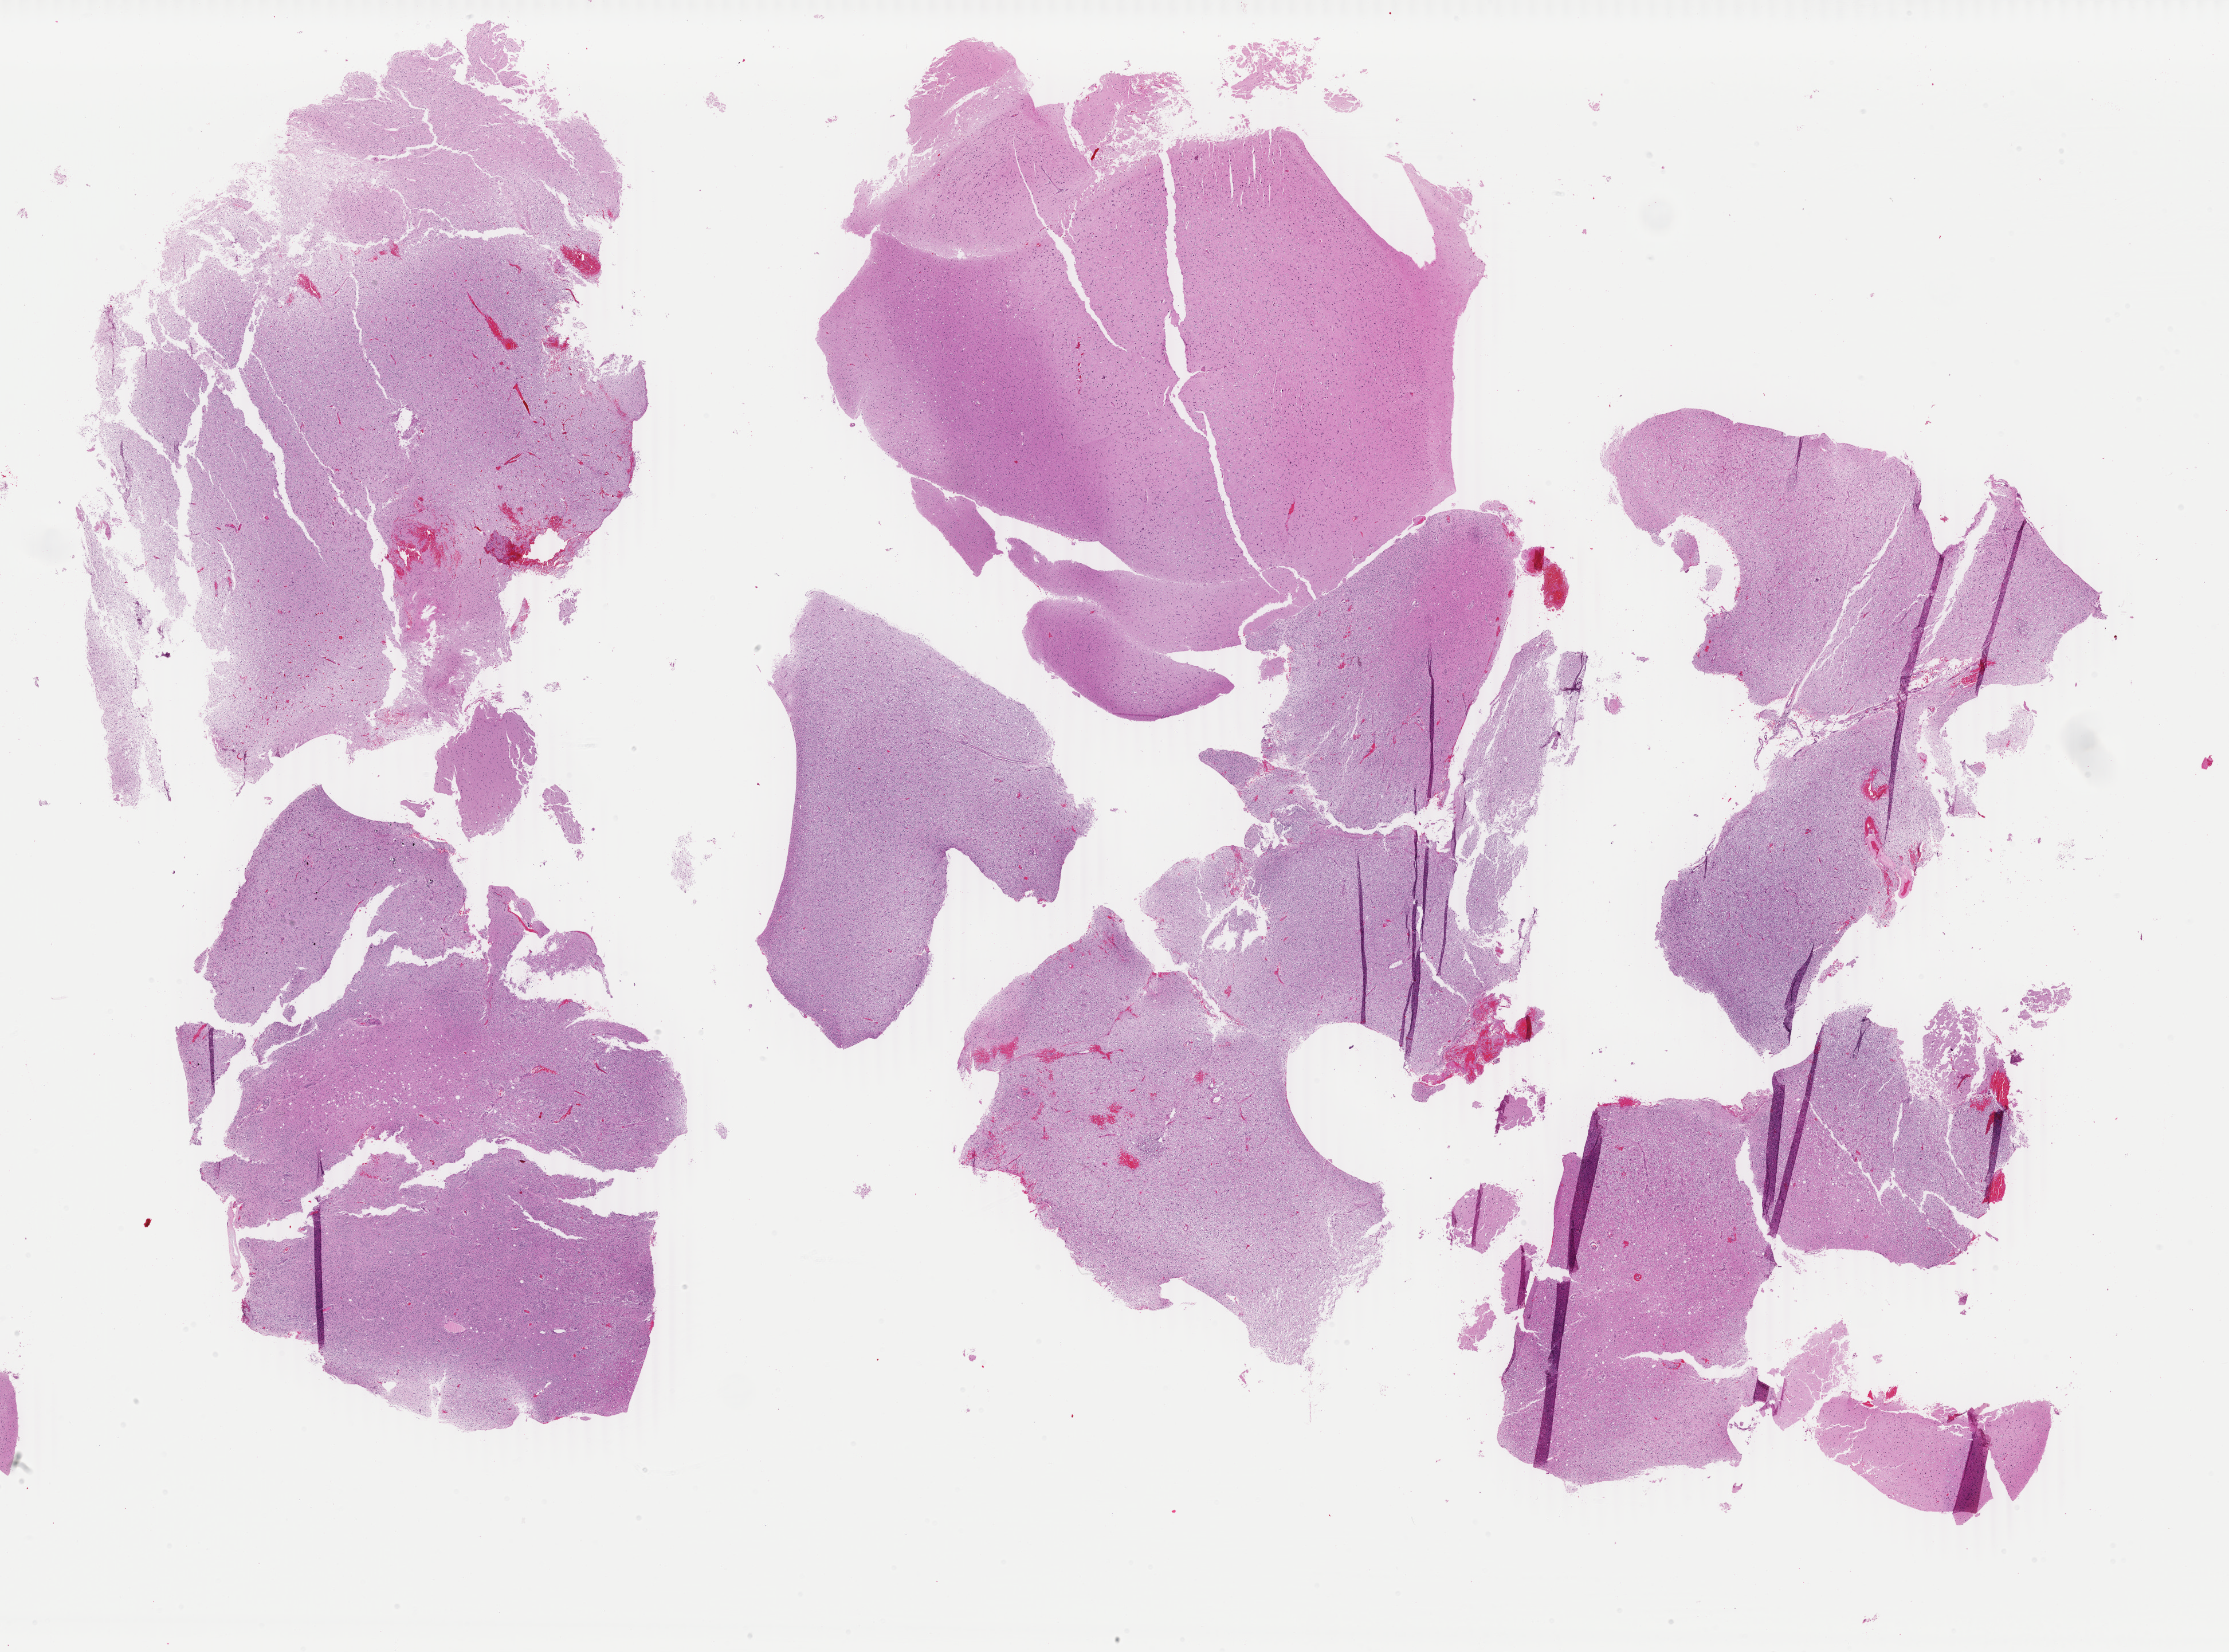
Hematoxylin and eosin (H&E) stained whole-slide image — whole scanned area (about 30.9 x 22.9 mm) shown as a low-resolution overview. Formalin-fixed paraffin-embedded (FFPE) diagnostic section. Brain, primary tumour sample. Patient: female, age at initial diagnosis 44 years. Histologic grade: G2 (moderately differentiated).
• diagnosis: Oligodendroglioma, NOS (cerebrum)